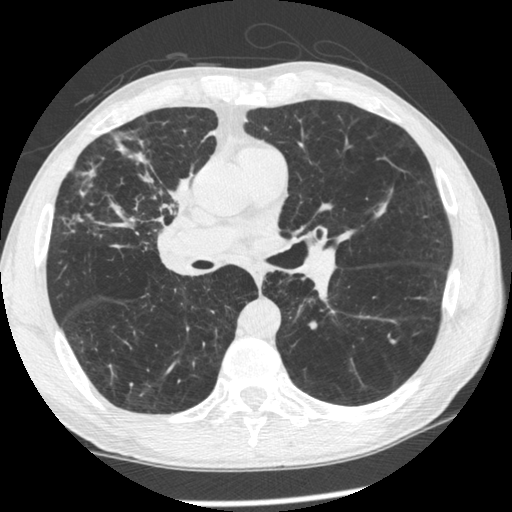
Low-dose screening chest CT, one axial slice. Slice 128 of 261 in the series (ordered by position). 120 kVp. Lung window (W 1500 / L -600 HU). 1.25 mm slice thickness. 512 × 512 image matrix, field of view 340 × 340 mm.
Structures marked on this image (manually delineated by an expert):
- lesion 1 (tumor, upper lobe of right lung): bounding box [x1, y1, x2, y2] px = [170, 173, 194, 205]